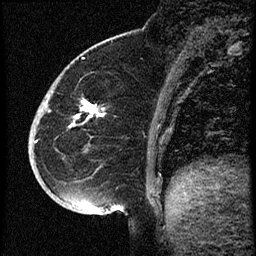
Breast MRI (dynamic contrast-enhanced), one sagittal slice. Slice 18 of 60 in the series (ordered by position). Dynamic contrast-enhanced study with each time point stored as its own series, time point 2 of 3 at this slice position (early post-contrast, ordered by acquisition time). 1.5 T. TE 4.2 ms, TR 18.9 ms. 2 mm slice thickness. 256 × 256 image matrix, field of view 200 × 200 mm. Female patient. From the clinical record (not read from this slice): setting: breast cancer imaged before/during neoadjuvant chemotherapy; receptor status: HR-positive, HER2-negative.
Structures marked on this image (semi-automatic segmentation, software-assisted and operator-edited):
- analysis volume of interest (the breast-tissue region the enhancement analysis was run in; not a lesion): bounding box [x1, y1, x2, y2] px = [30, 87, 106, 173]
- tumour enhancement mask (voxels above the 100 % enhancement threshold inside the analysis volume of interest): [86, 104, 103, 117]